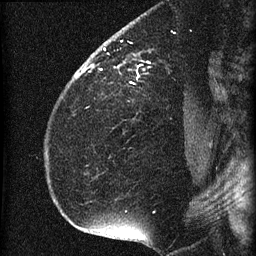
Breast MRI (dynamic contrast-enhanced), one sagittal slice. Dynamic contrast-enhanced series, image 2 of 4 at this slice position (ordered by acquisition). 1.5 T. TE 4.2 ms, TR 22.7 ms. 256 × 256 image matrix, field of view 180 × 180 mm. Patient: female, 35 years. From the clinical record (not read from this slice): setting: breast cancer imaged before/during neoadjuvant chemotherapy; receptor status: HR-positive, HER2-negative.
Structures marked on this image (semi-automatic segmentation, software-assisted and operator-edited):
- analysis volume of interest (the breast-tissue region the enhancement analysis was run in; not a lesion): bounding box [x1, y1, x2, y2] px = [69, 27, 199, 112]
- tumour enhancement mask (voxels above the 90 % enhancement threshold inside the analysis volume of interest): [75, 48, 150, 78]